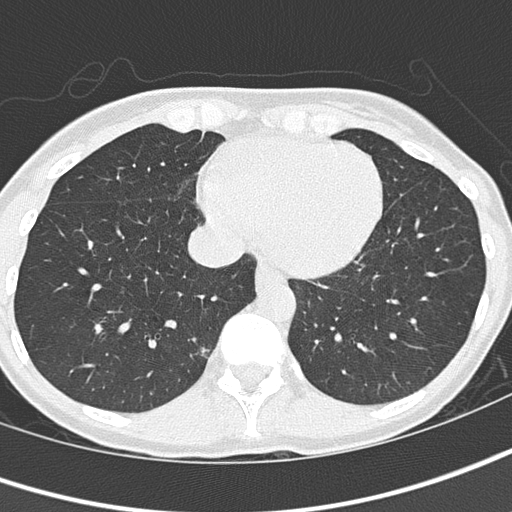
Chest CT (low-dose screening protocol), one axial image; baseline annual screen; lung window (W 1500 / L -600 HU). Female participant, aged 57 years at enrolment. Current smoker at enrolment.
Lesion marked by an expert reader, bounding box [x1, y1, x2, y2] px = [185, 336, 221, 367]. The exam's reader record, not a measurement of the box and not confirmed to be the same lesion: non-calcified nodule or mass ≥4 mm, right lower lobe, 11 × 6 mm, mixed attenuation. Official screen result: positive, change unspecified: nodule(s) >= 4 mm or enlarging nodule(s), mass(es), or other non-specific abnormalities suspicious for lung cancer. Lung cancer was diagnosed 61 days after this screen: adenocarcinoma, NOS, right lower lobe, moderately differentiated (G2), stage IA (AJCC 6th edition), 8 mm at pathology.